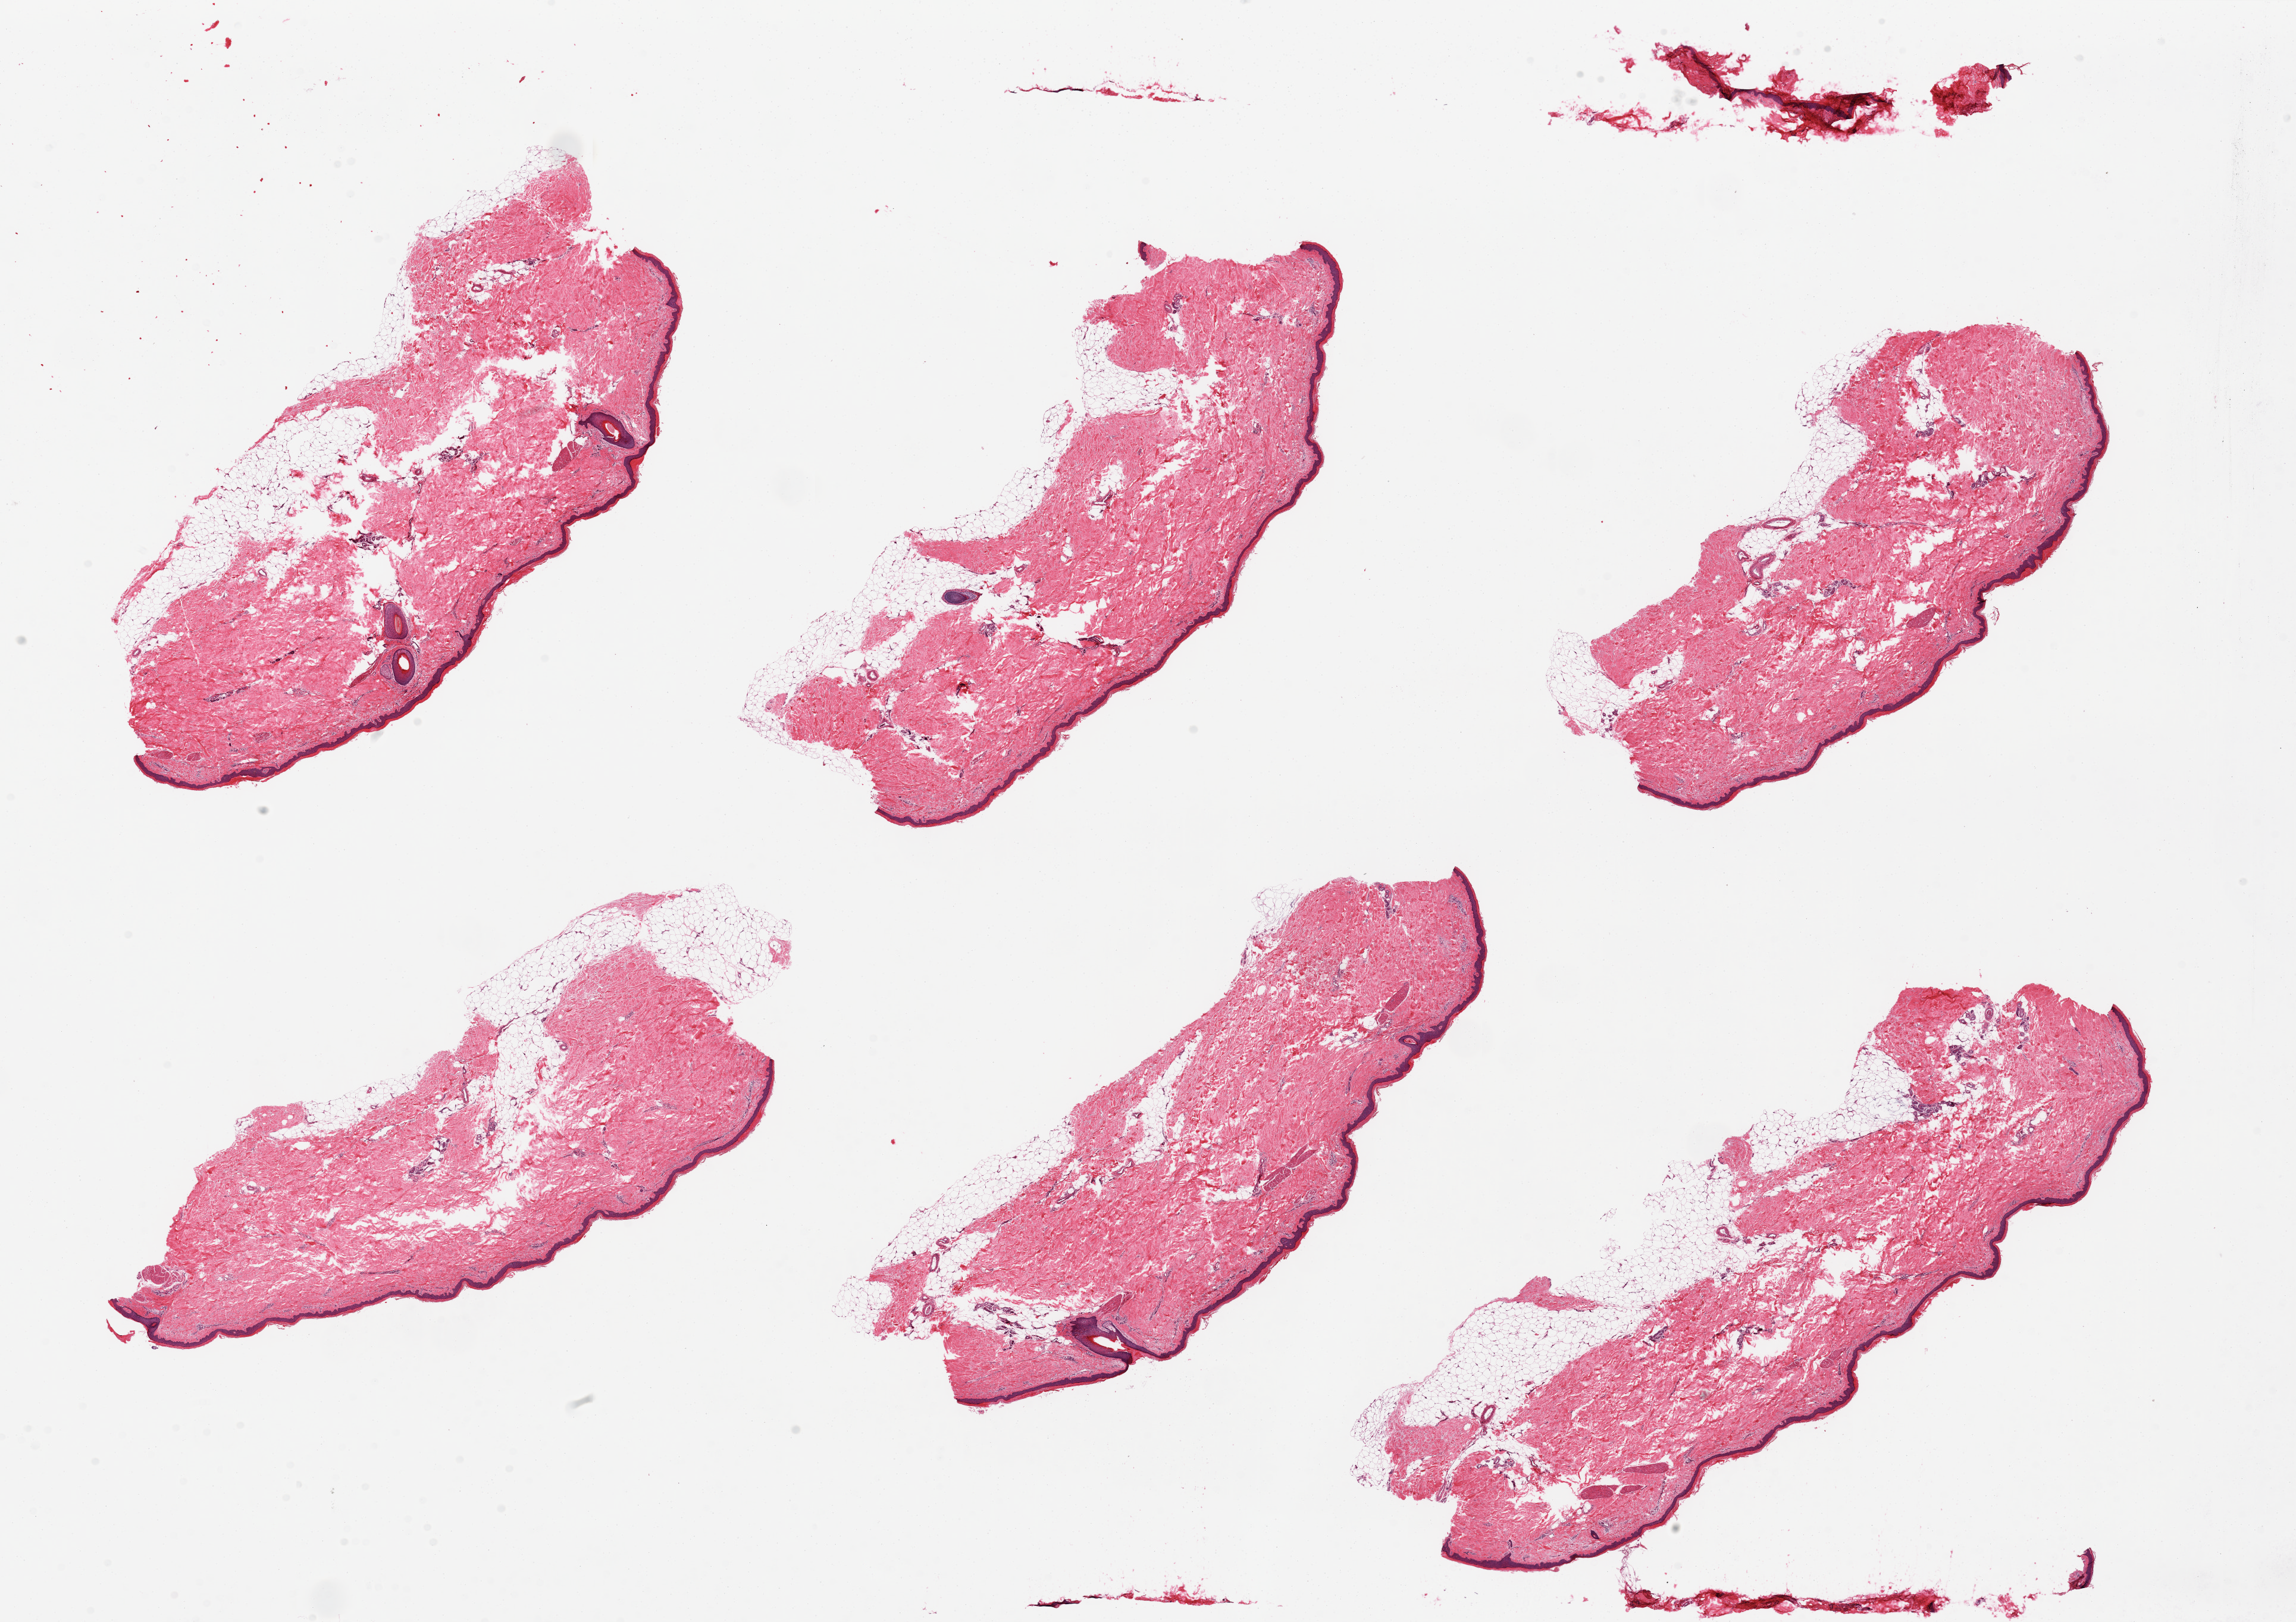
Hematoxylin and eosin (H&E) whole-slide image, whole scanned area (about 30.5 x 21.6 mm) shown as a low-resolution overview; PAXgene-fixed paraffin-embedded (PFPE) section; sampled site (target tissue): skin of lower leg; tissue donor sample. Donor sex: male.
Reviewer comment on this tissue sample: 6 pieces, several with 10-30% predominantly attached adipose tissue, squamous epithelium is ~45-50 microns thick.